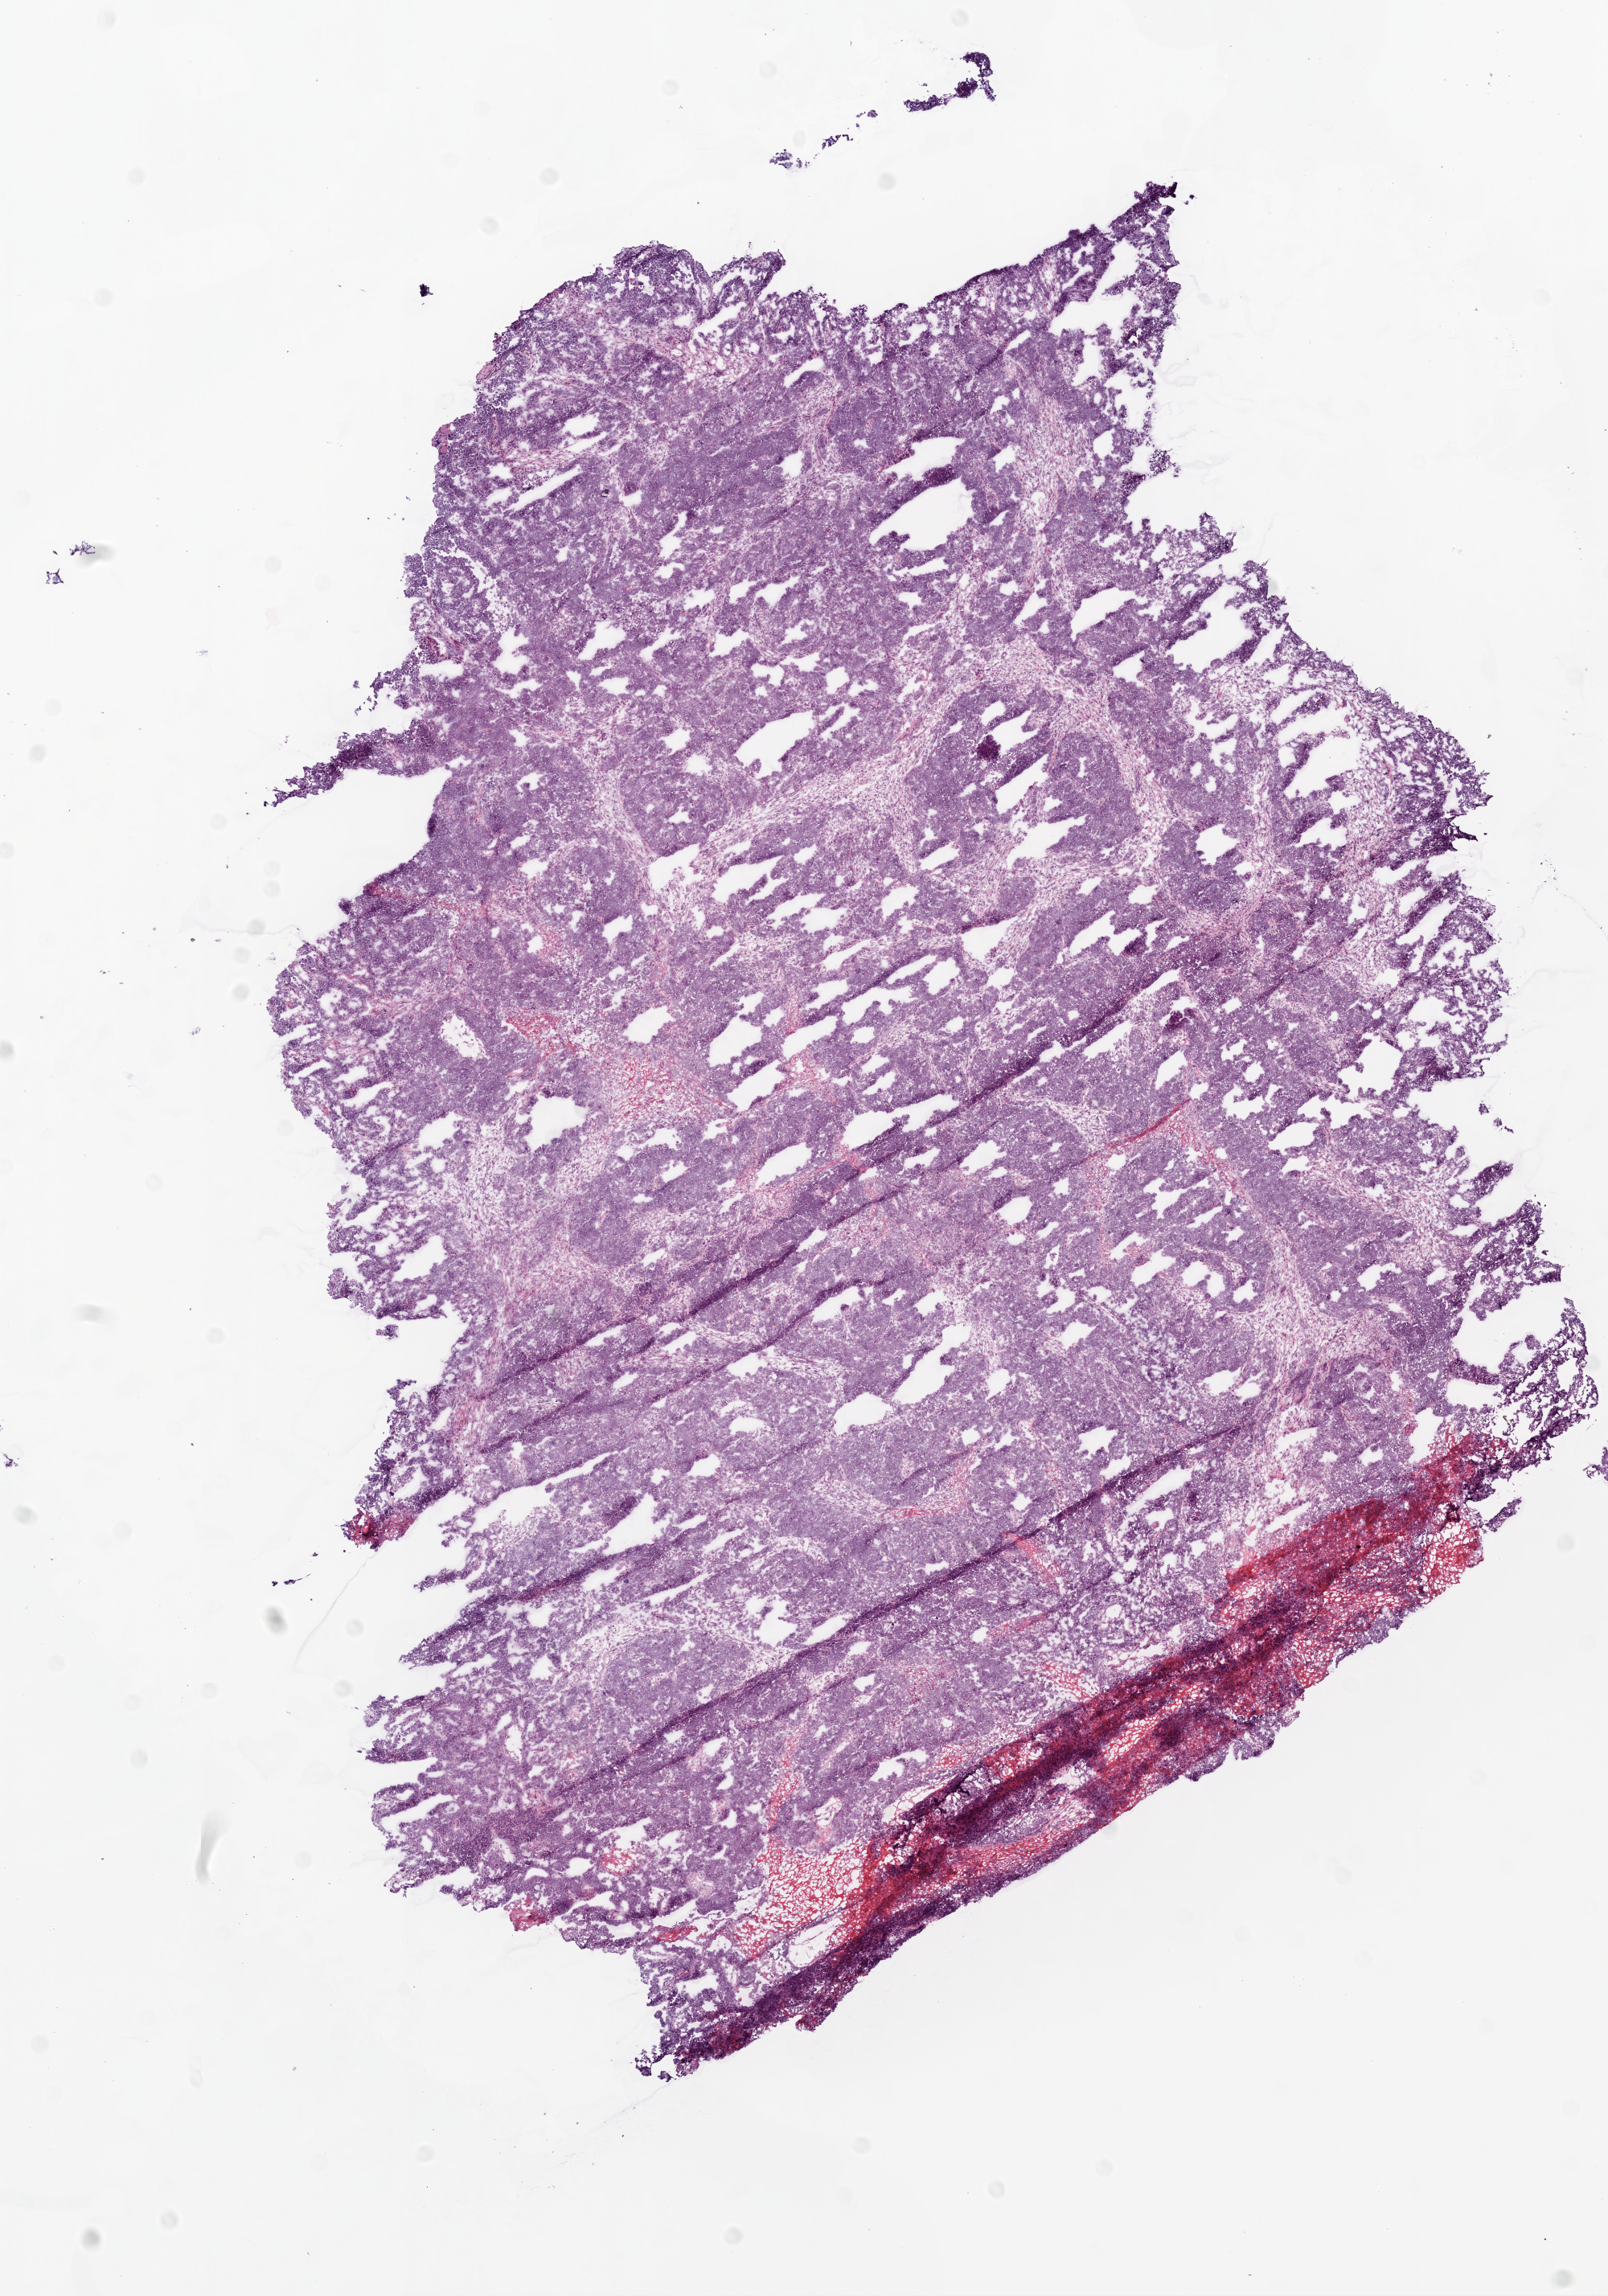
Digitized H&E-stained tissue section (whole slide) — low-resolution overview of the scanned area, about 8.0 x 11.5 mm (slide scanned at 20x). Frozen section from the bottom of the tissue portion. Sample: primary tumour, ovary. Patient: female, age at initial diagnosis 52 years. Histologic grade: G3 (poorly differentiated). Pathologist review of this section (percent, as recorded): tumour cells 90%, tumour nuclei 95%, normal cells 0%, stromal cells 10%, necrosis 0%. Inflammatory infiltration, as recorded: lymphocyte infiltration 3%.
Diagnosis: Serous cystadenocarcinoma, NOS. FIGO stage: IIIC.